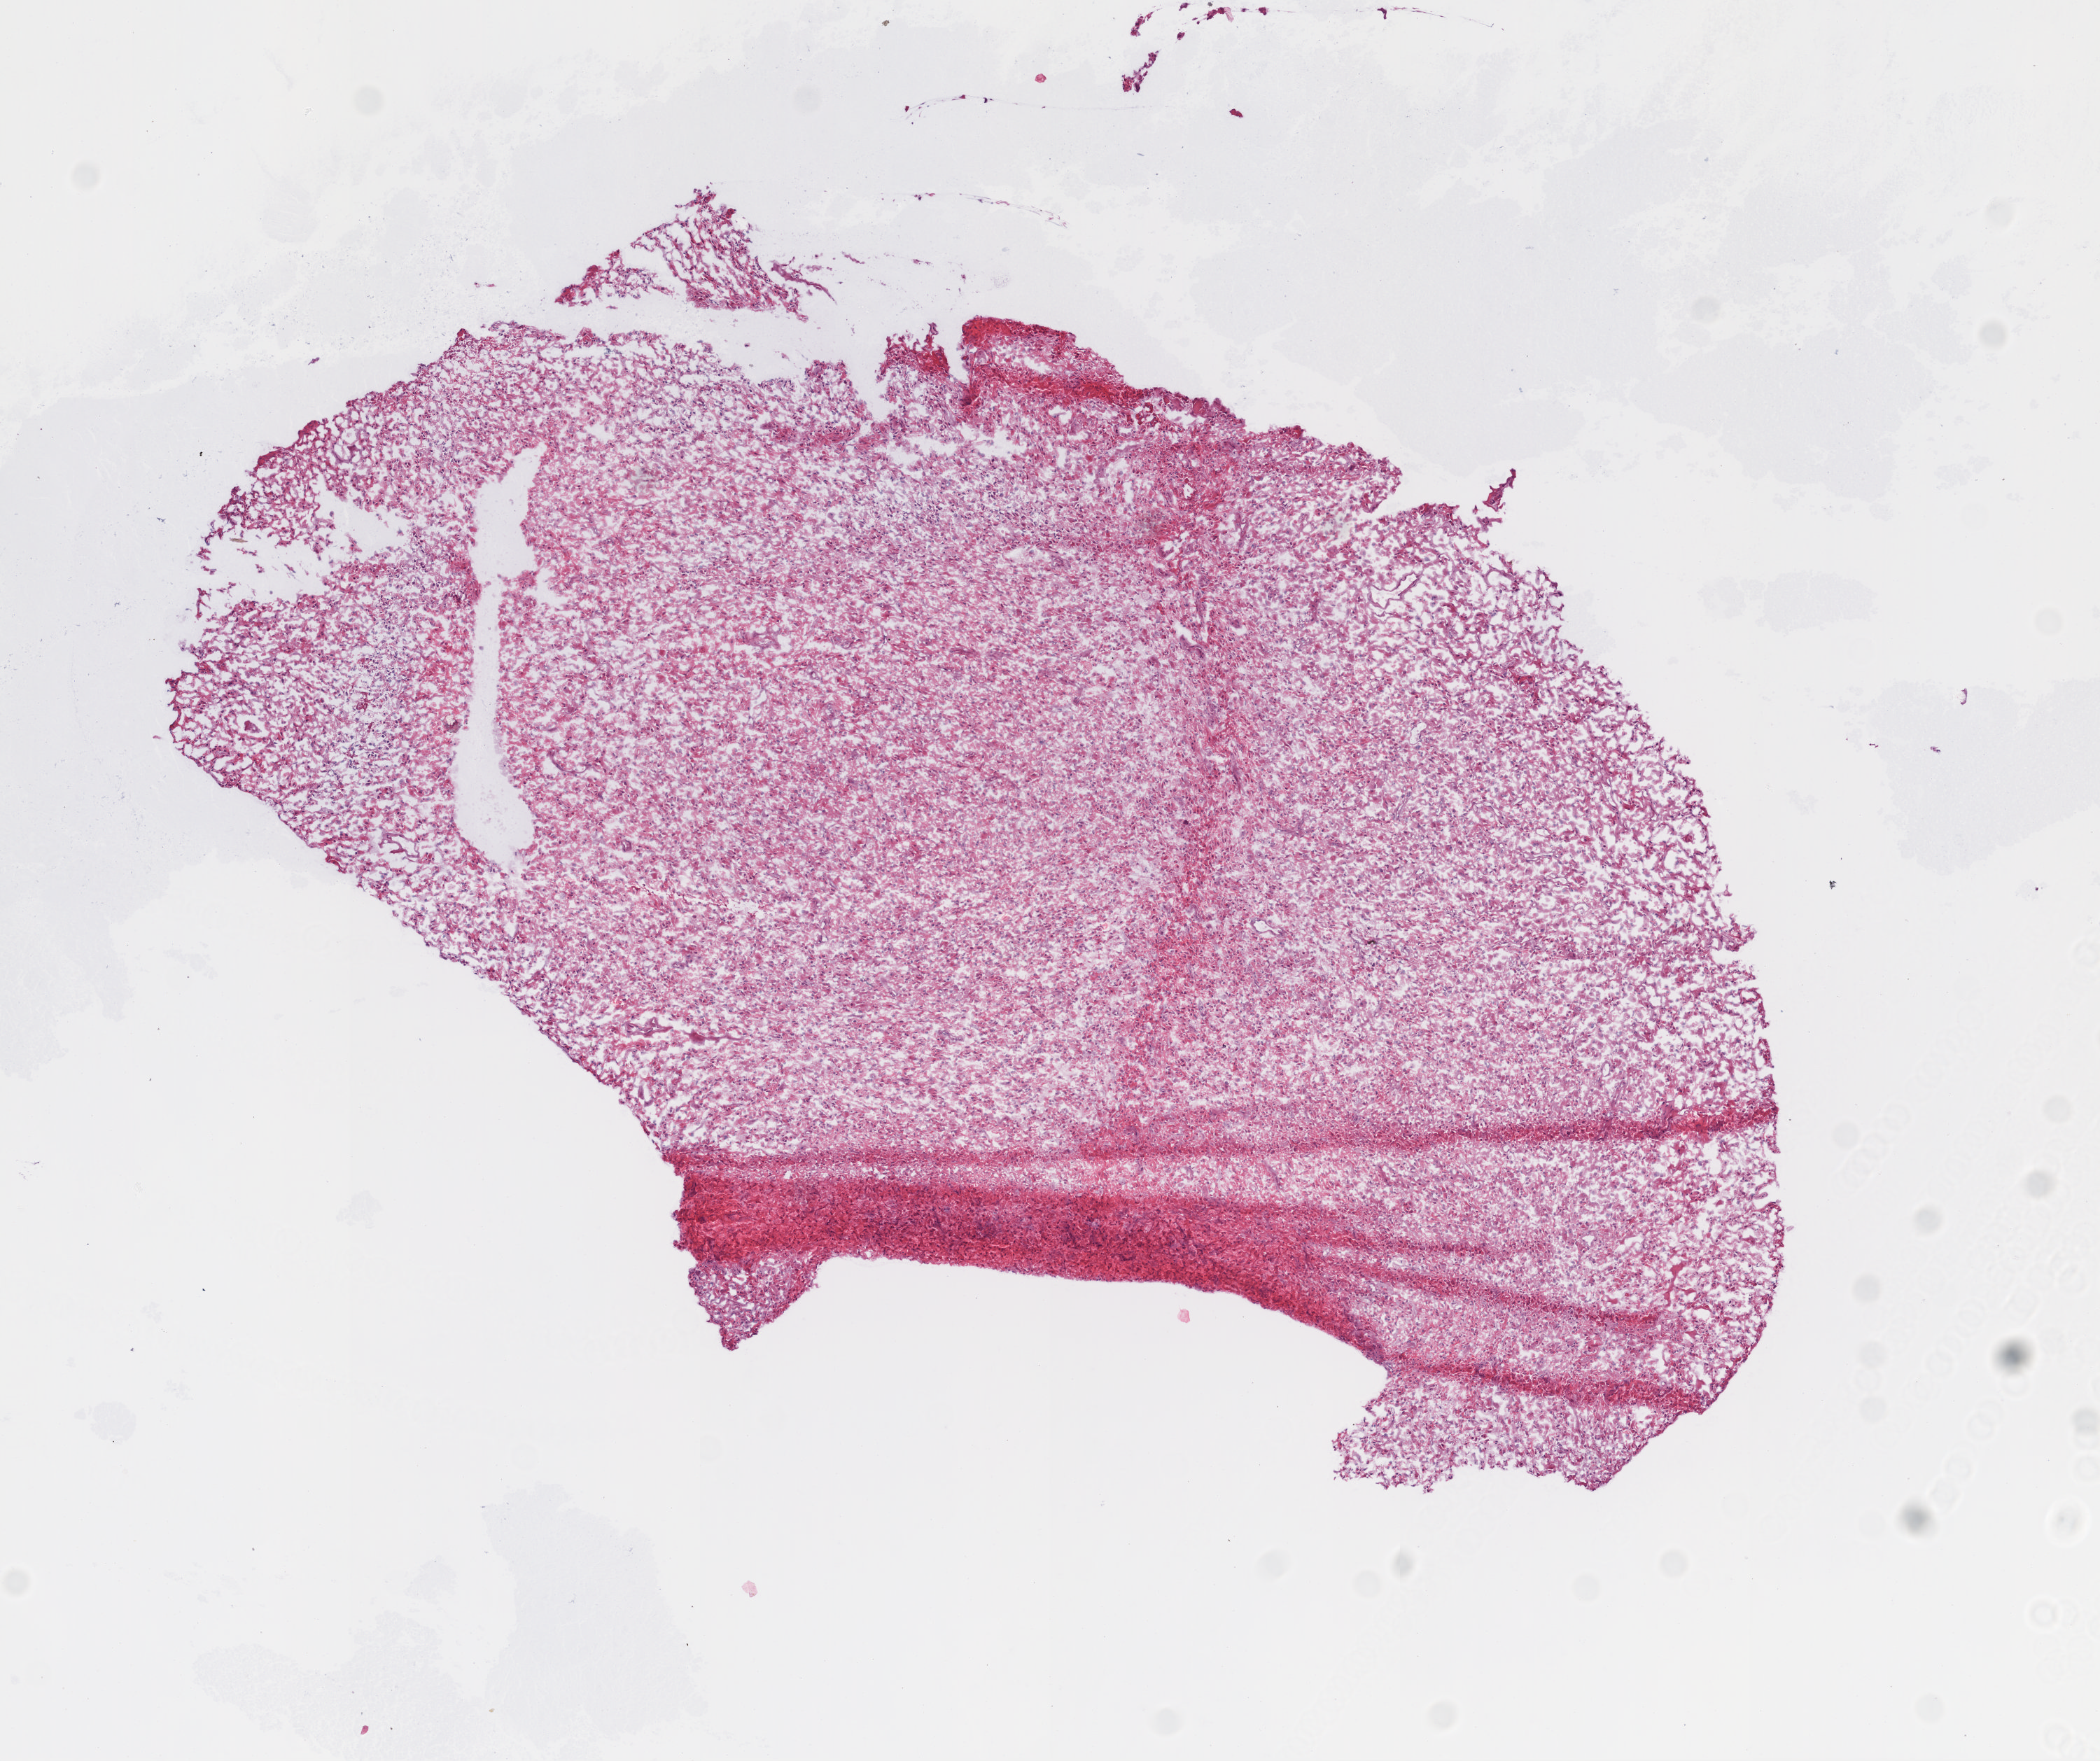
Digitized H&E tissue section (whole slide) — whole scanned area (about 6.0 x 5.0 mm) shown as a low-resolution overview; frozen section; primary tumour sample from the brain. Male patient; age at initial diagnosis 59 years. Composition of this section per pathologist review: tumour cells 99%, tumour nuclei 80%, normal cells 0%, stromal cells 0%, necrosis 1%.
- diagnosis: Glioblastoma